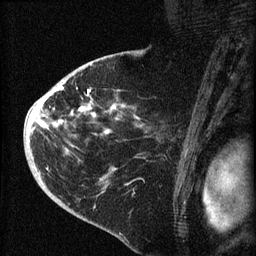
Breast MRI (dynamic contrast-enhanced), one sagittal slice. Position 45 of 60 along the scan axis. Dynamic contrast-enhanced series, image 2 of 4 at this slice position (ordered by acquisition). 1.5 T. TE 4.2 ms, TR 8.2 ms. 2 mm slice thickness. 256 × 256 image matrix, field of view 180 × 180 mm. Patient: female, 71 years.
Annotated regions visible in this slice (semi-automatic segmentation, software-assisted and operator-edited):
- analysis volume of interest (the breast-tissue region the enhancement analysis was run in; not a lesion): box from (x=35, y=75) to (x=148, y=190) px
- tumour enhancement mask (voxels above the 70 % enhancement threshold inside the analysis volume of interest): (x=35, y=81)–(x=138, y=134)